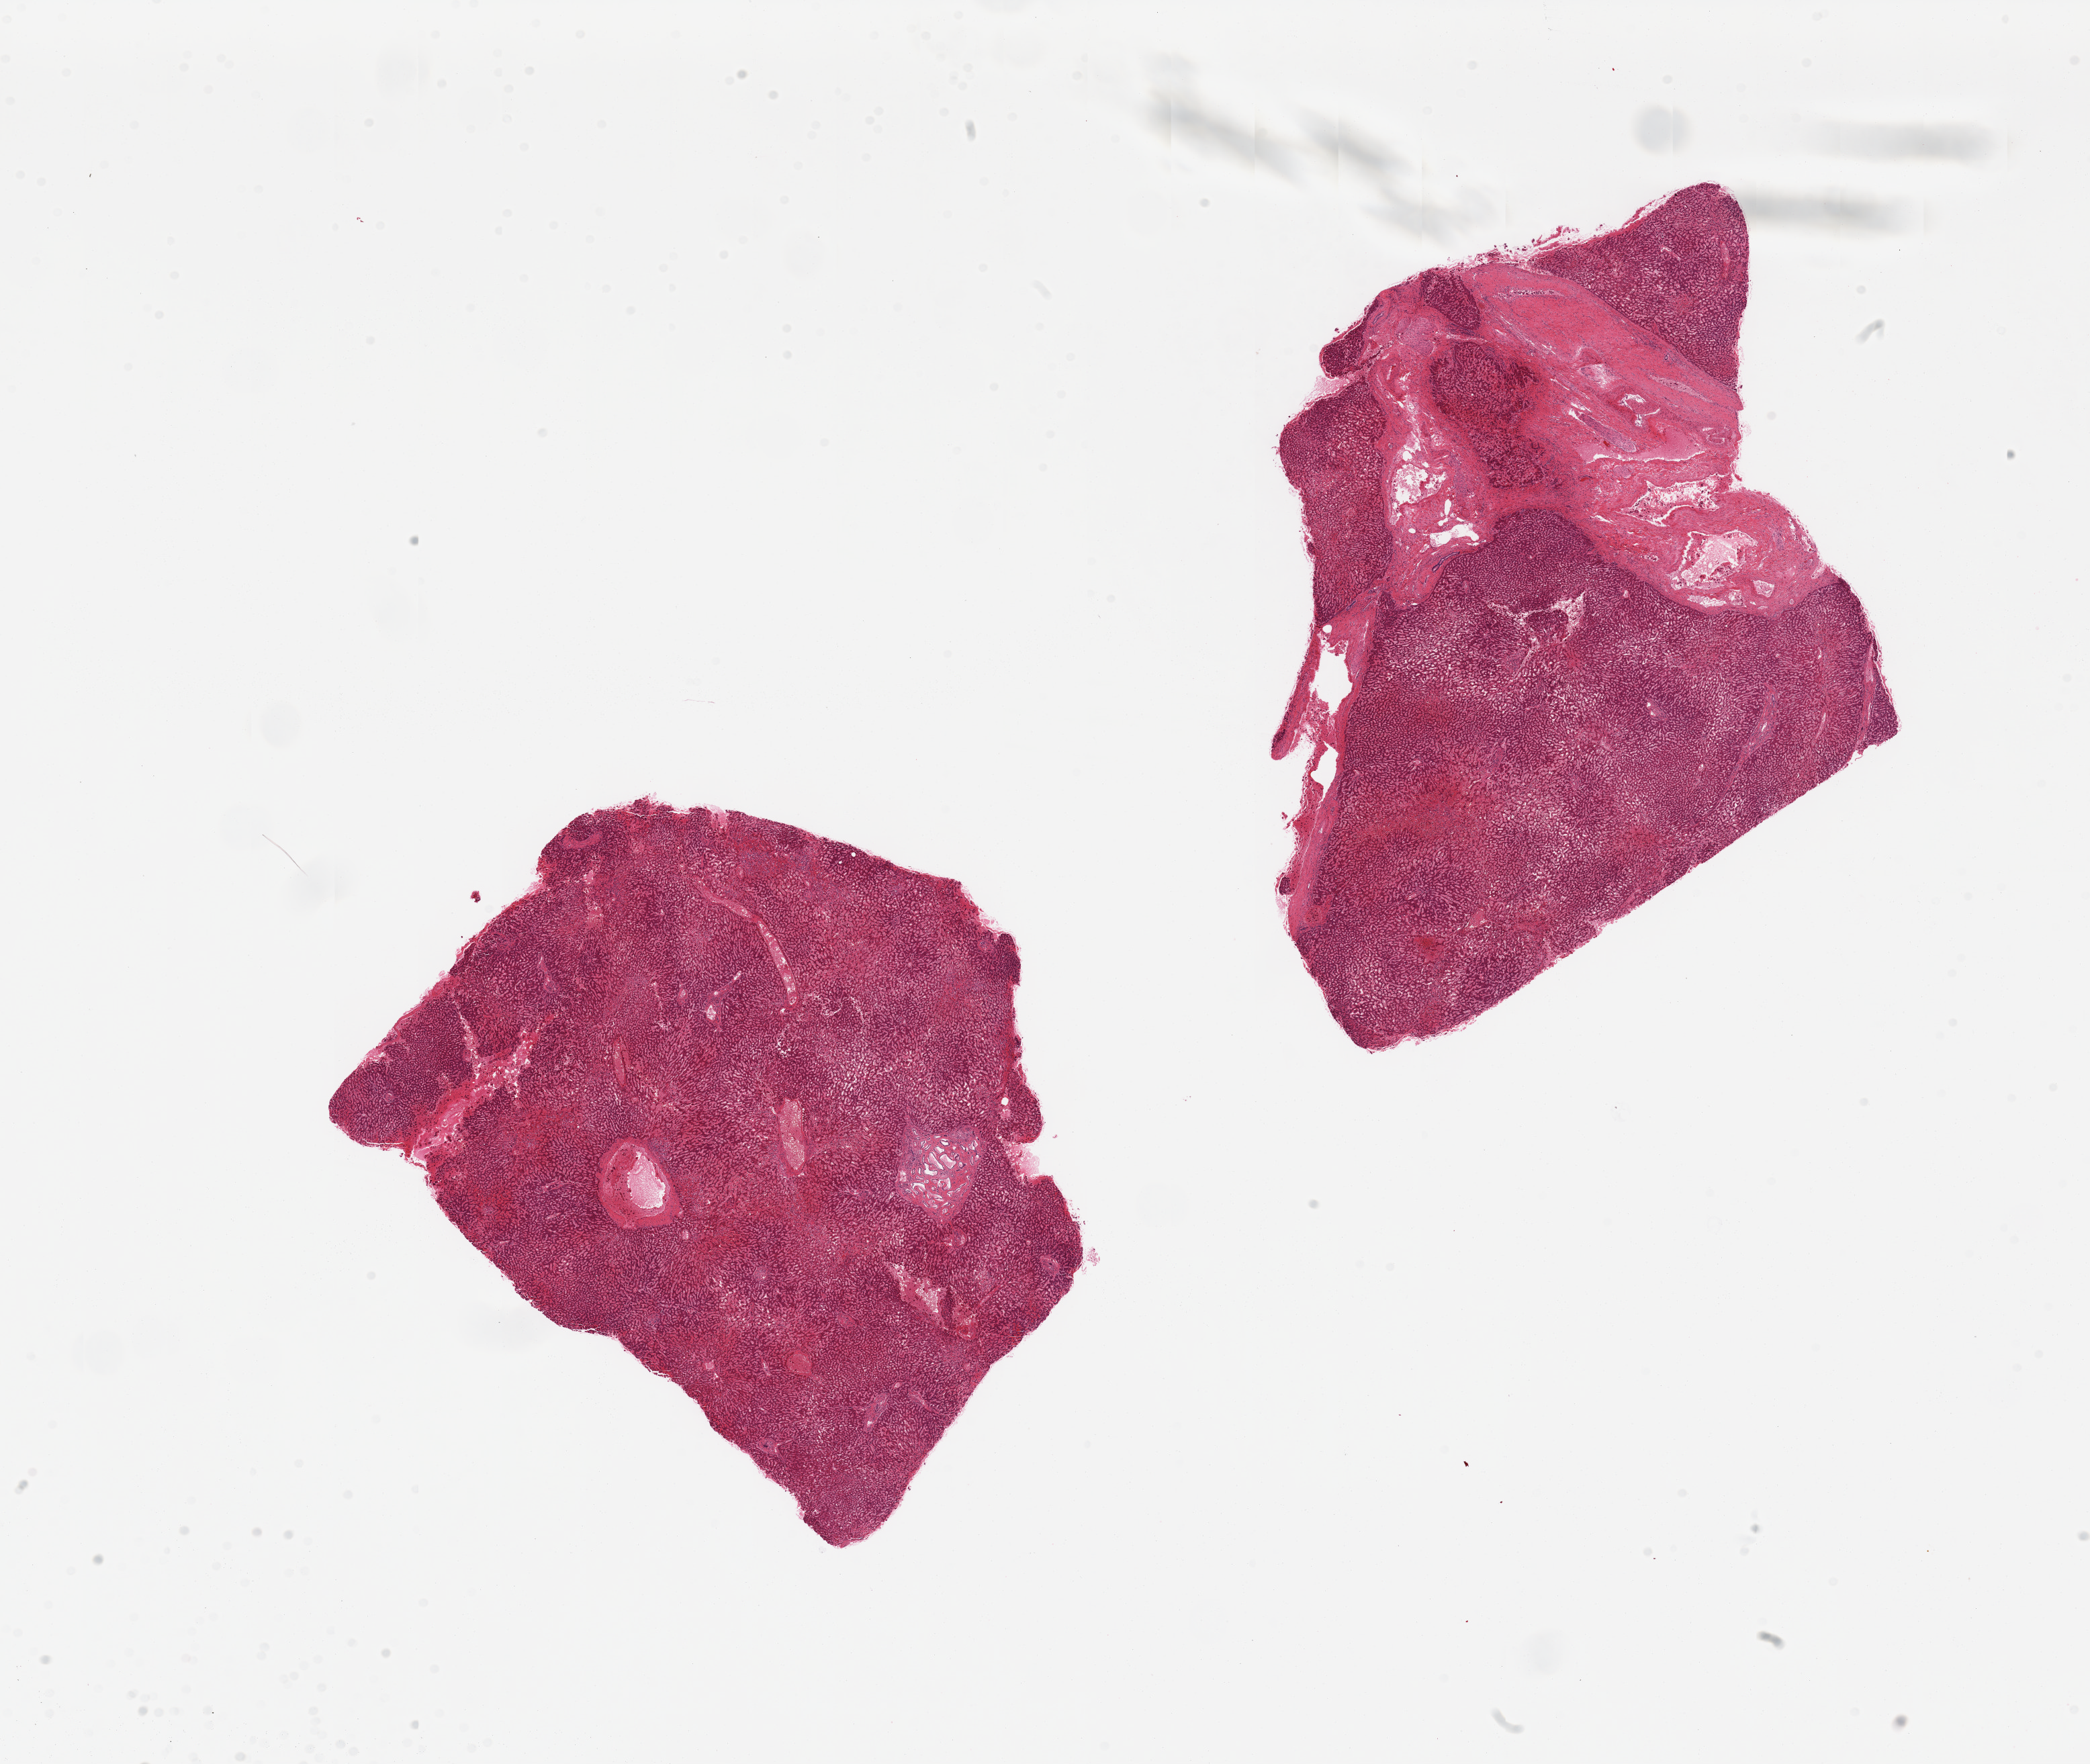
Whole-slide image, hematoxylin and eosin (H&E) stain — shown as a low-resolution overview of the whole scanned area (about 24.6 x 20.8 mm, acquisition: 20x scan), PAXgene-fixed, paraffin-embedded tissue, target tissue: liver, donor tissue sample.
Pathologist's review note for this sample: 2 pieces; moderately congested; 30% fibrovascular focus in 1 piece; 1 mm von Meyenberg complex in 2nd piece.